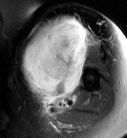
MRI of an extremity soft-tissue mass, one axial slice; position 49 of 87 along the scan axis; T2-weighted fat-saturated; MR volume resampled by the dataset authors to the PET/CT grid (not the native acquisition matrix); 3.27 mm slice thickness; 127 × 138 image matrix, field of view 124 × 135 mm. Female patient. Case-level facts recorded for this patient, not image findings: histological type: pleiomorphic leiomyosarcoma; grade: high; site of the primary tumour: left biceps.
Structures marked on this image (expert contour drawn on MRI and transferred to this co-registered scan by the dataset authors):
- gross tumour volume including surrounding oedema: bounding box [x1, y1, x2, y2] px = [22, 16, 94, 110]
- gross tumour volume (mass): [22, 18, 89, 104]